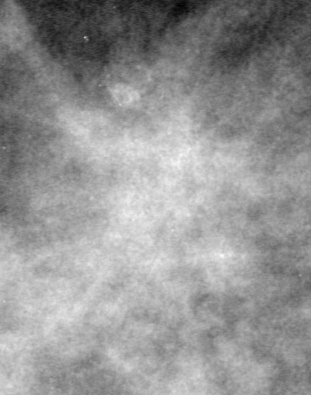
Cropped region of a digitized screen-film mammogram centred on a radiologist-marked abnormality; left breast; MLO view.
- Finding: mass, shape irregular, margins spiculated; BI-RADS assessment category 4; subtlety rating 1 on a 1 (subtle) to 5 (obvious) scale; pathology (as recorded): malignant.